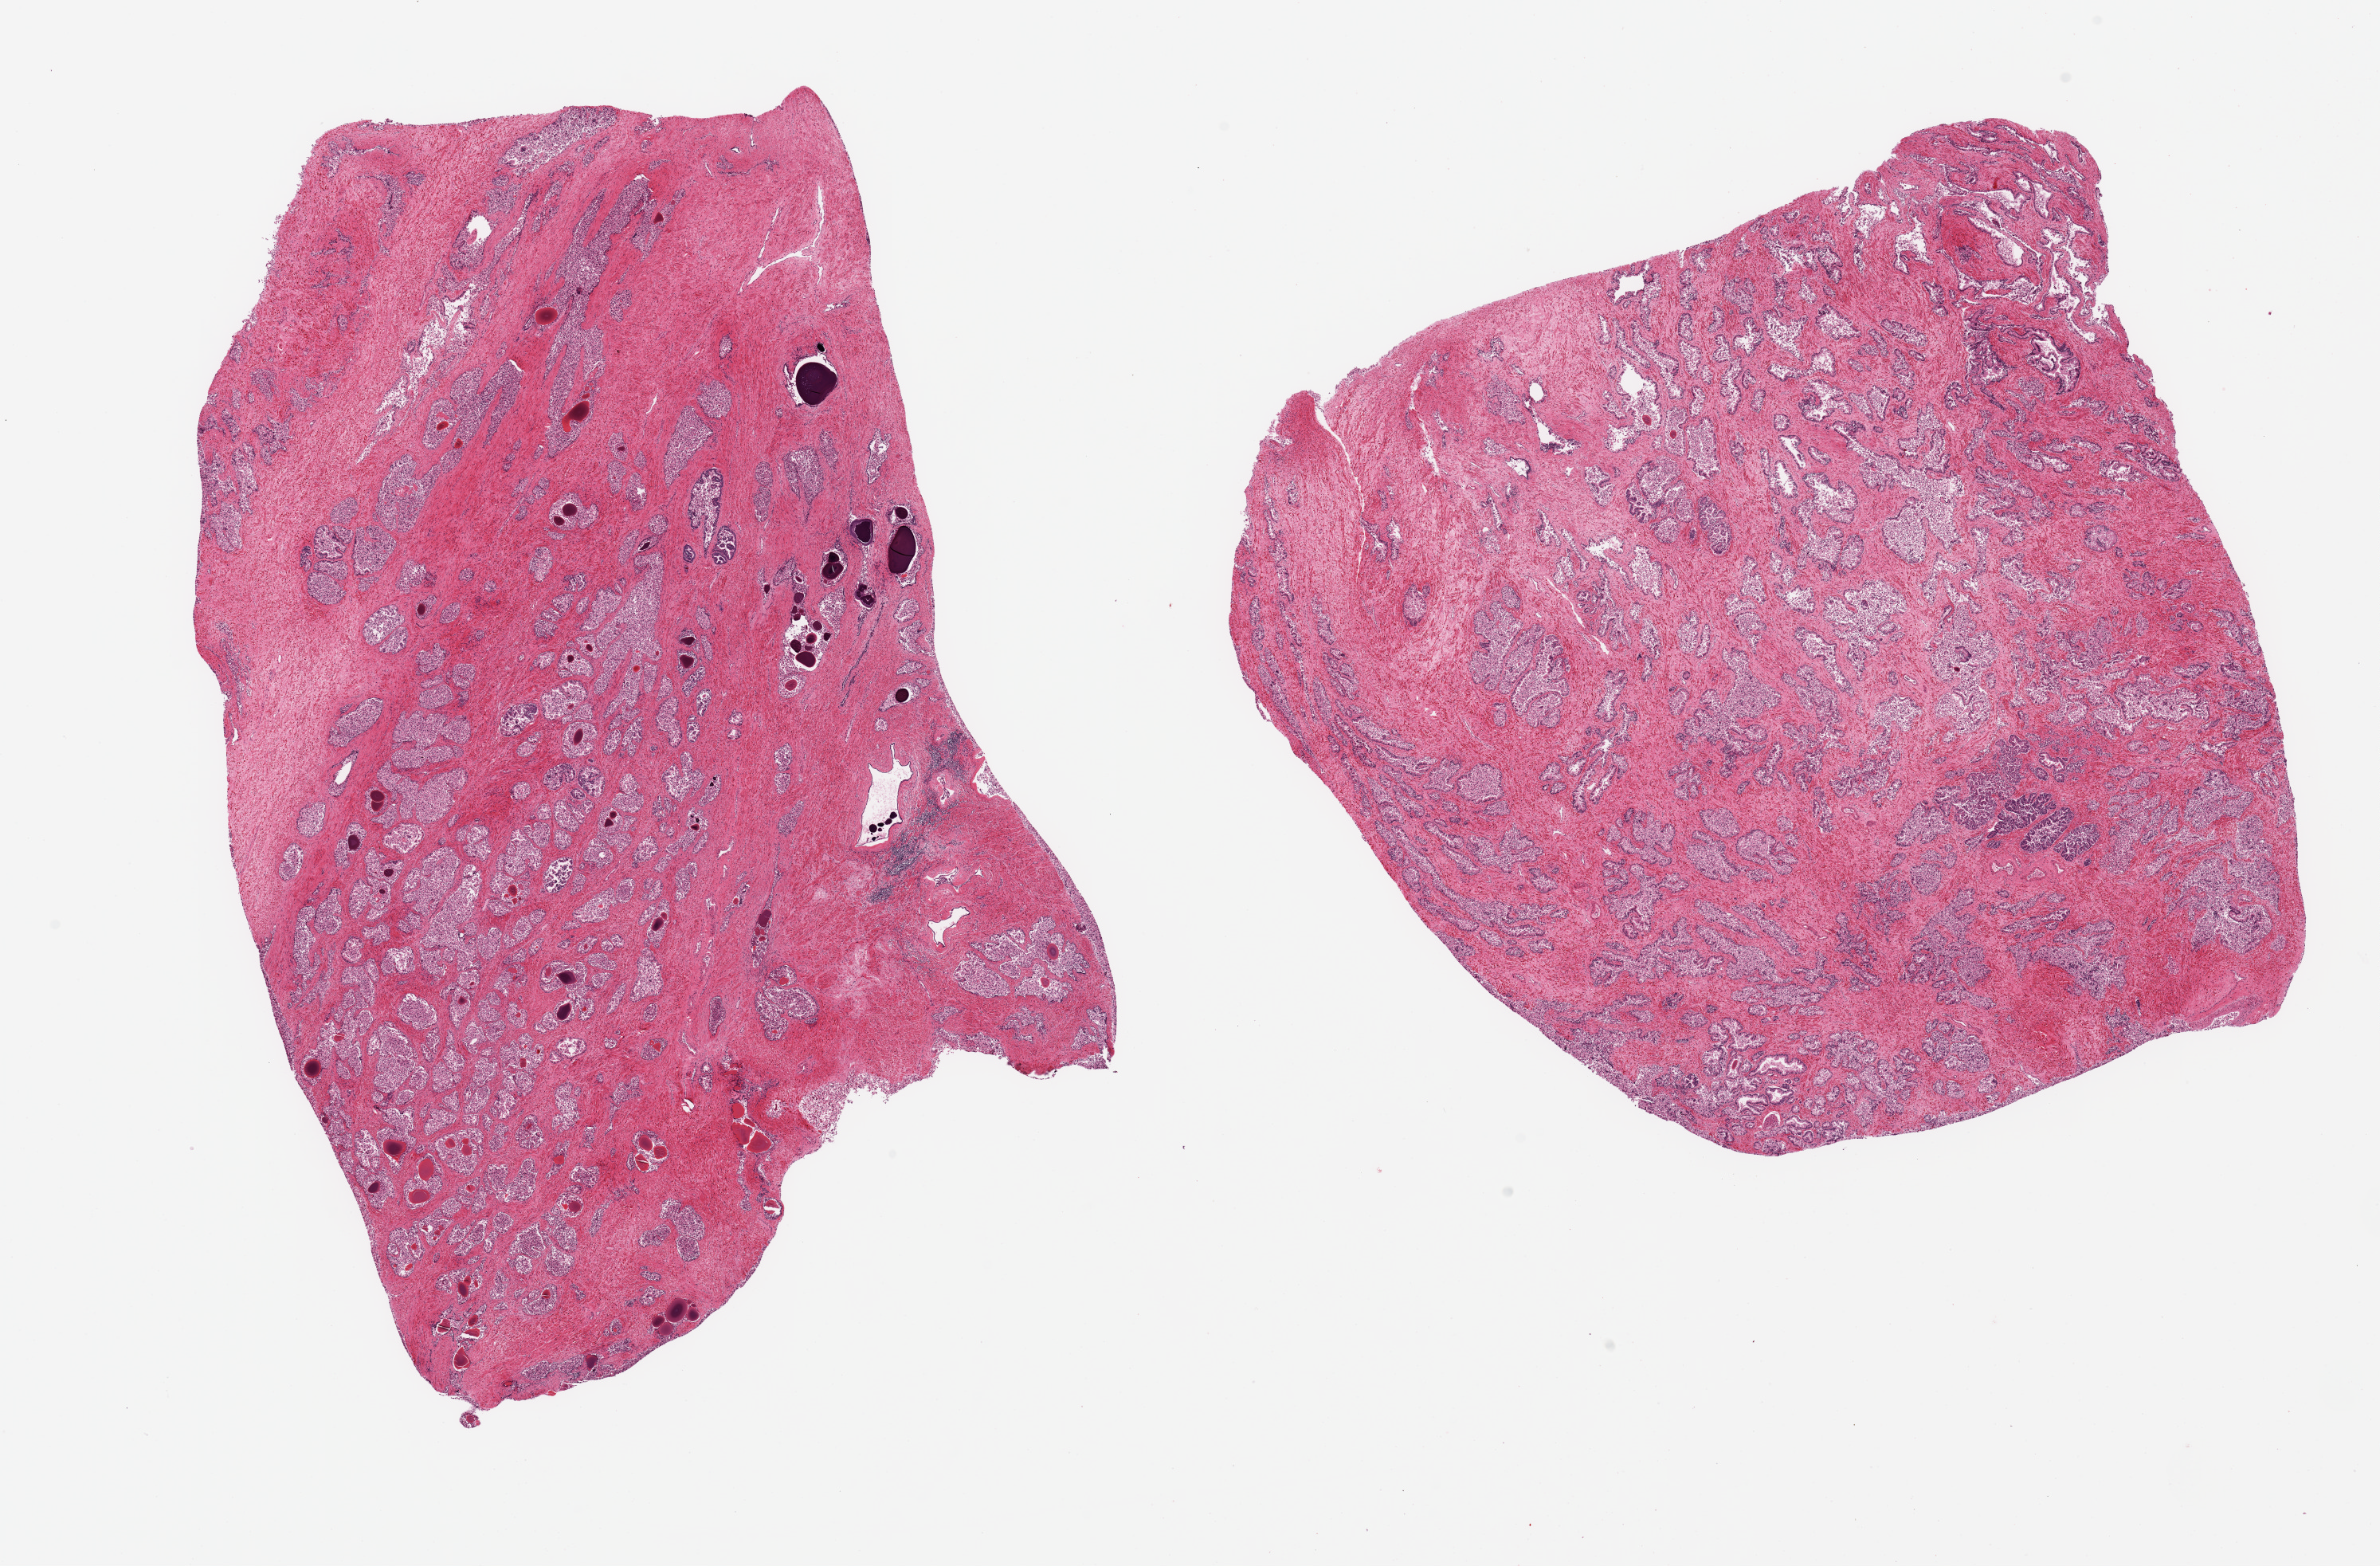
Hematoxylin and eosin (H&E) whole-slide image, brightfield — low-resolution overview of the scanned area, about 23.6 x 15.5 mm (from a 20x scan); PAXgene-fixed paraffin-embedded (PFPE) section; sampled site (target tissue): prostate; donor tissue sample. Male donor.
Review note (as recorded): 2 pieces, diffuse predominately advanced glandular autolysis; hyperplastic pattern.